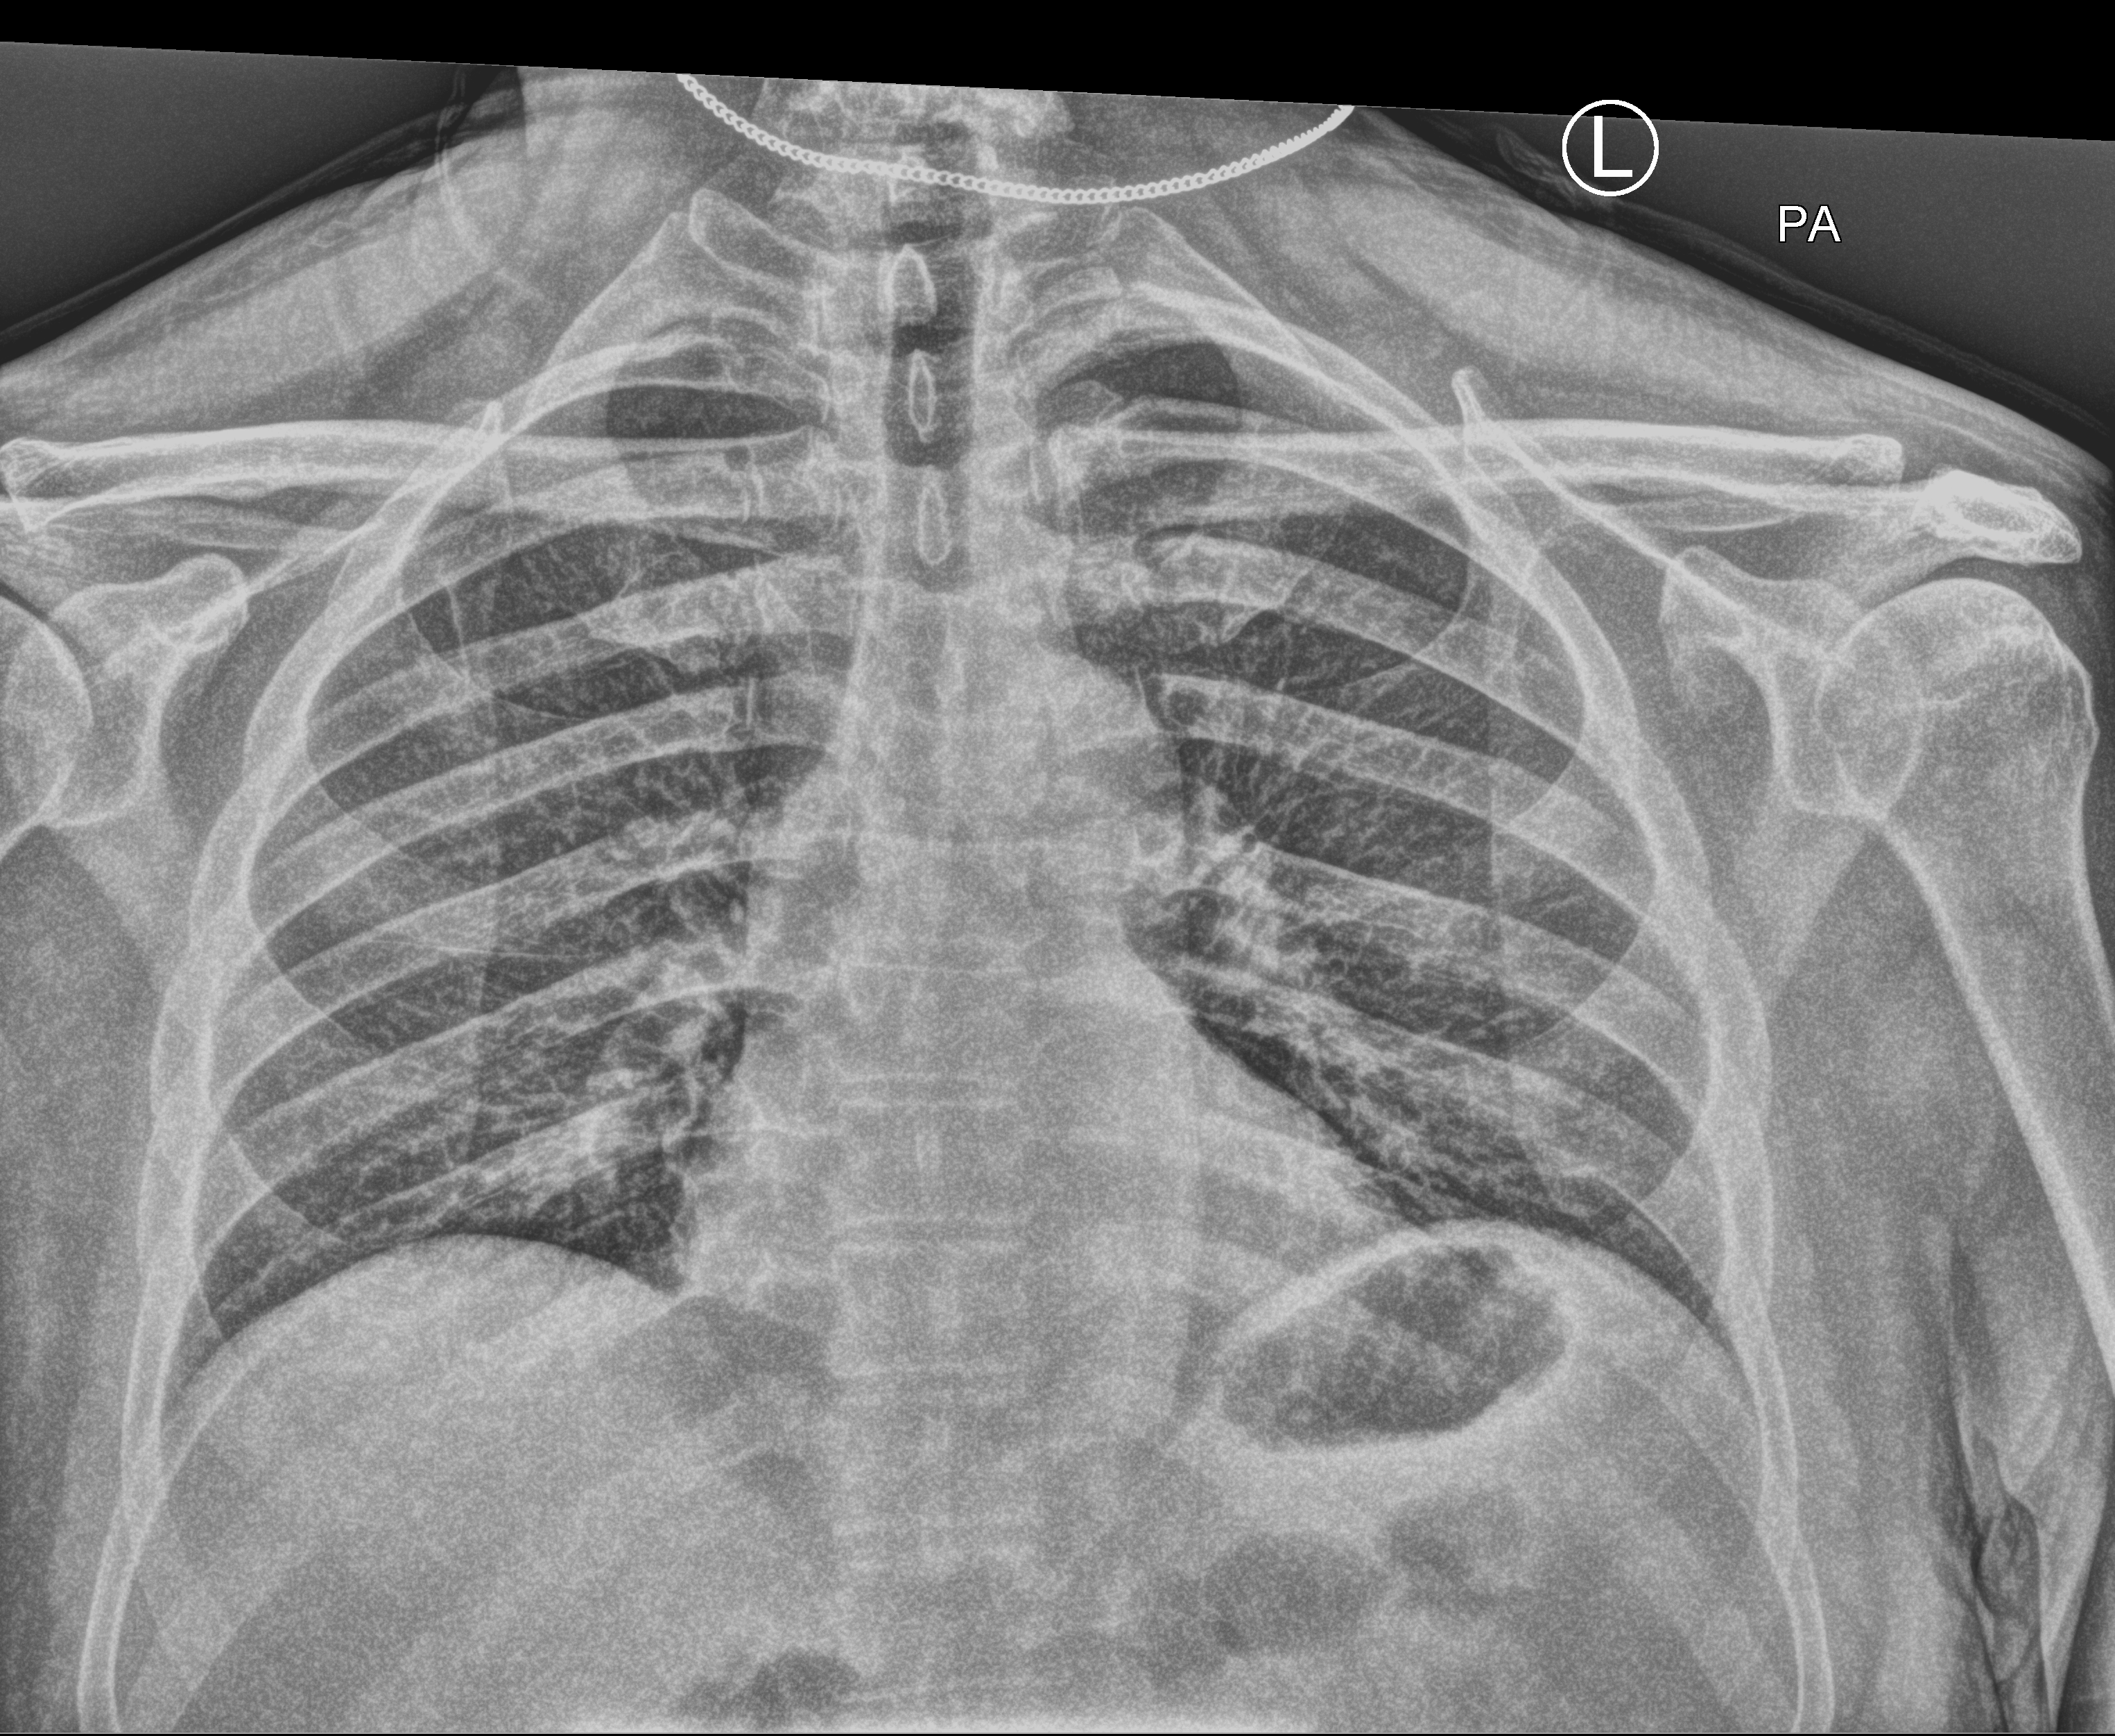
Chest X-ray (portable); anteroposterior (AP) projection. Patient hospitalised with COVID-19; male, aged 60–74 years.
Hospital-stay facts (about this admission, not read from this image; timing relative to this image not recorded): mechanically ventilated during this hospital stay: no.